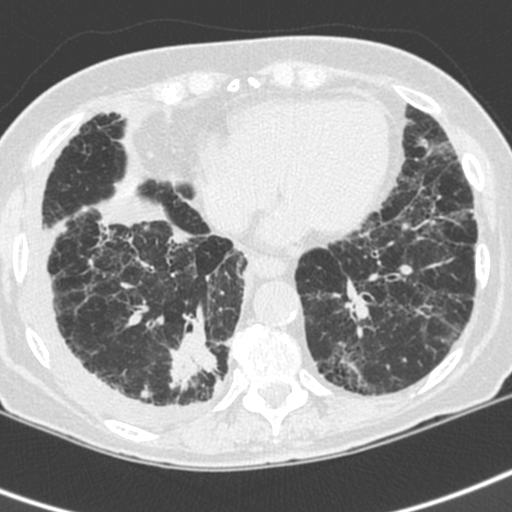
Chest CT (low-dose screening protocol), one axial image. First (baseline) screen. Lung window (W 1500 / L -600 HU). 1.3 mm slice thickness. Standard (soft-tissue) reconstruction kernel (C). Slice 134 of 192 in the series. 512 × 512 image matrix, field of view 288 × 288 mm. Female, age 73 years at enrolment. Current smoker at enrolment.
Expert-annotated lung lesion, box from (x=155, y=316) to (x=235, y=406) px. The exam's reader record, not a measurement of the box and not confirmed to be the same lesion: non-calcified nodule or mass ≥4 mm, right lower lobe, 35 × 30 mm, spiculated (stellate) margins, soft tissue attenuation. Official screen result: positive, change unspecified: nodule(s) >= 4 mm or enlarging nodule(s), mass(es), or other non-specific abnormalities suspicious for lung cancer. Later outcome: lung cancer diagnosed 22 days after this screen — adenocarcinoma, NOS, right lower lobe, stage IV (AJCC 6th edition), 35 mm at pathology.